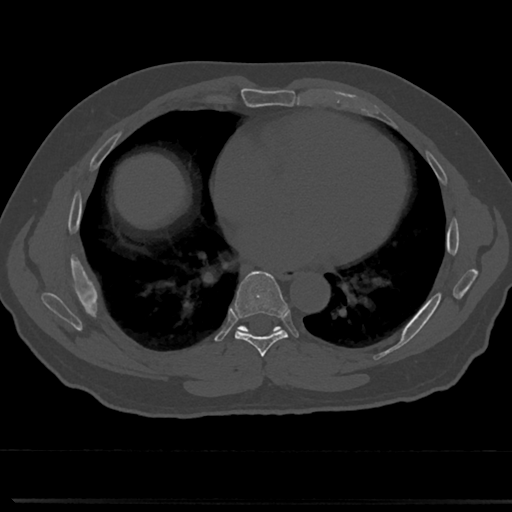
CT including the spine, one axial slice; position 394 of 817 along the scan axis; reconstruction kernel Br40s/3; 120 kVp; bone window (W 1800 / L 400 HU); 0.5 mm slice thickness; 512 × 512 image matrix, field of view 355 × 355 mm. Patient: male, 61 years. Case-level facts recorded for this patient, not image findings: primary cancer: prostate.
Outlined on this slice (semi-automatically segmented with operator editing):
- T6 vertebra: bounding box (x1, y1, x2, y2) in pixels: (261, 353, 269, 377)
- T7 vertebra: (214, 275, 310, 357)